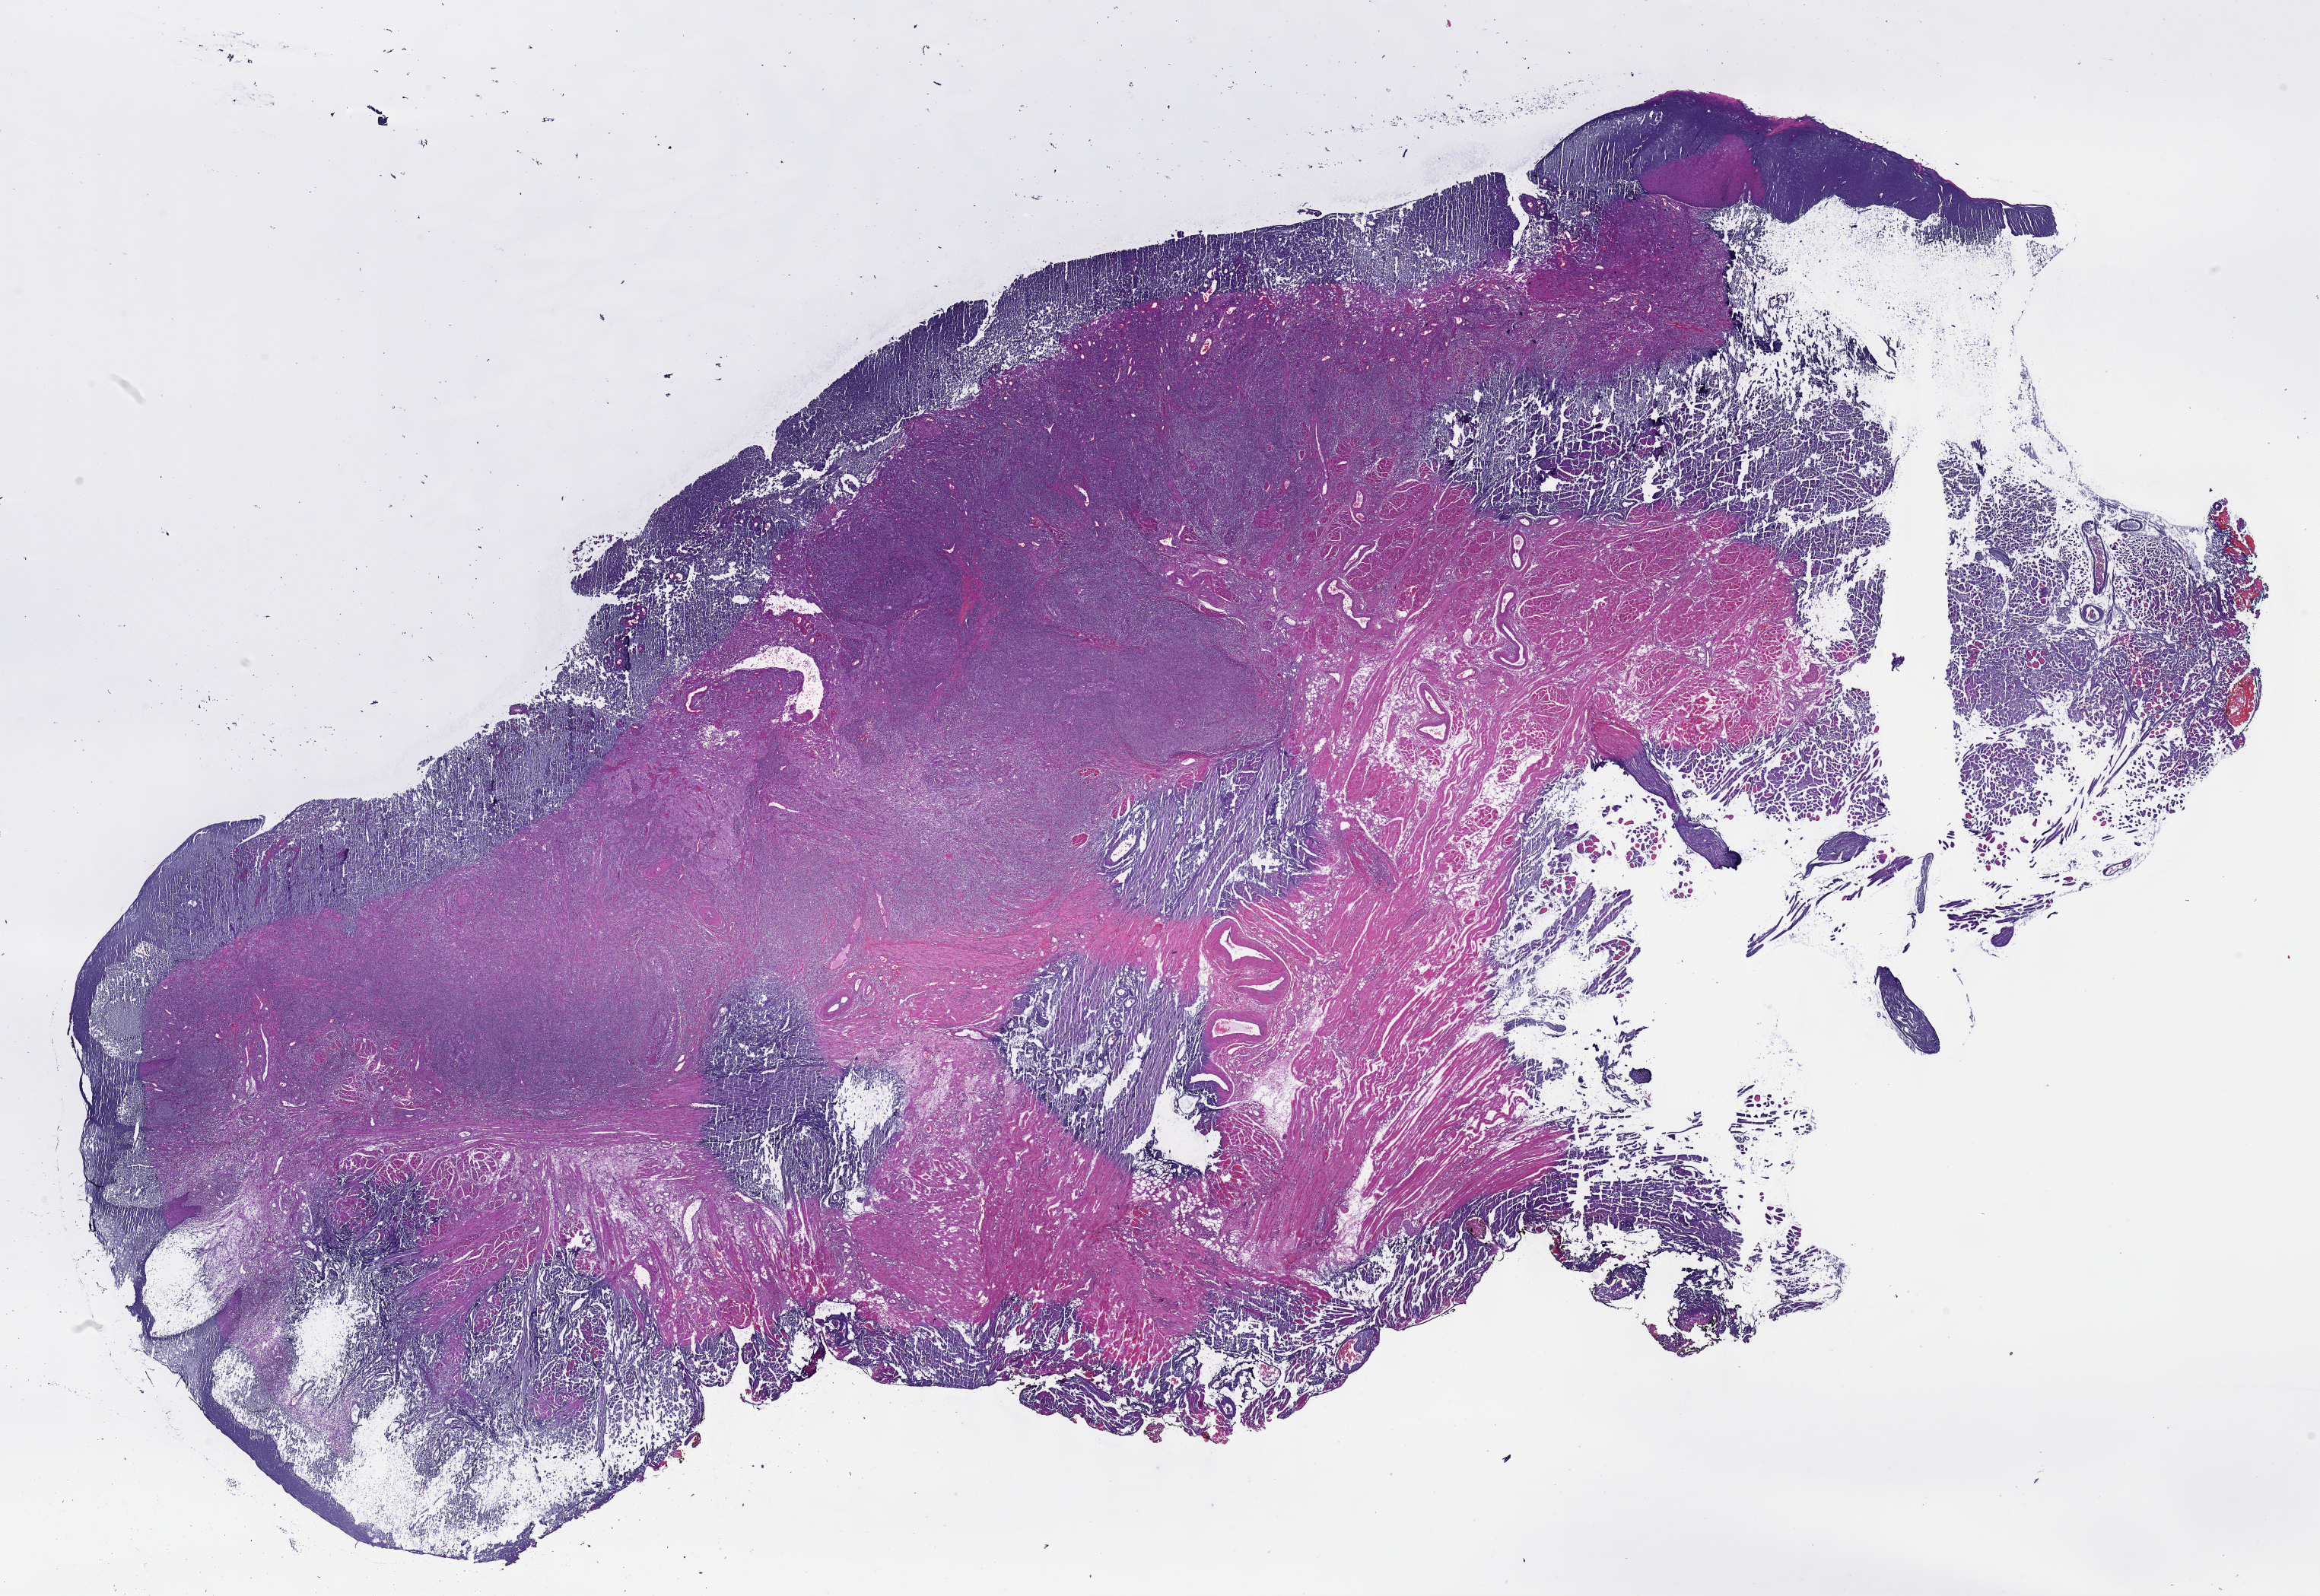
Whole-slide histology image, H&E-stained — a low-resolution overview of the entire scanned area, about 24.6 x 17.0 mm (acquisition: 40x scan). Formalin-fixed paraffin-embedded (FFPE) diagnostic section. Primary tumour sample from the head and neck. Patient: female, age at initial diagnosis 64 years. Histologic grade: G3 (poorly differentiated).
Laterality: right. Pathologic diagnosis: Squamous cell carcinoma, NOS (tongue, NOS).